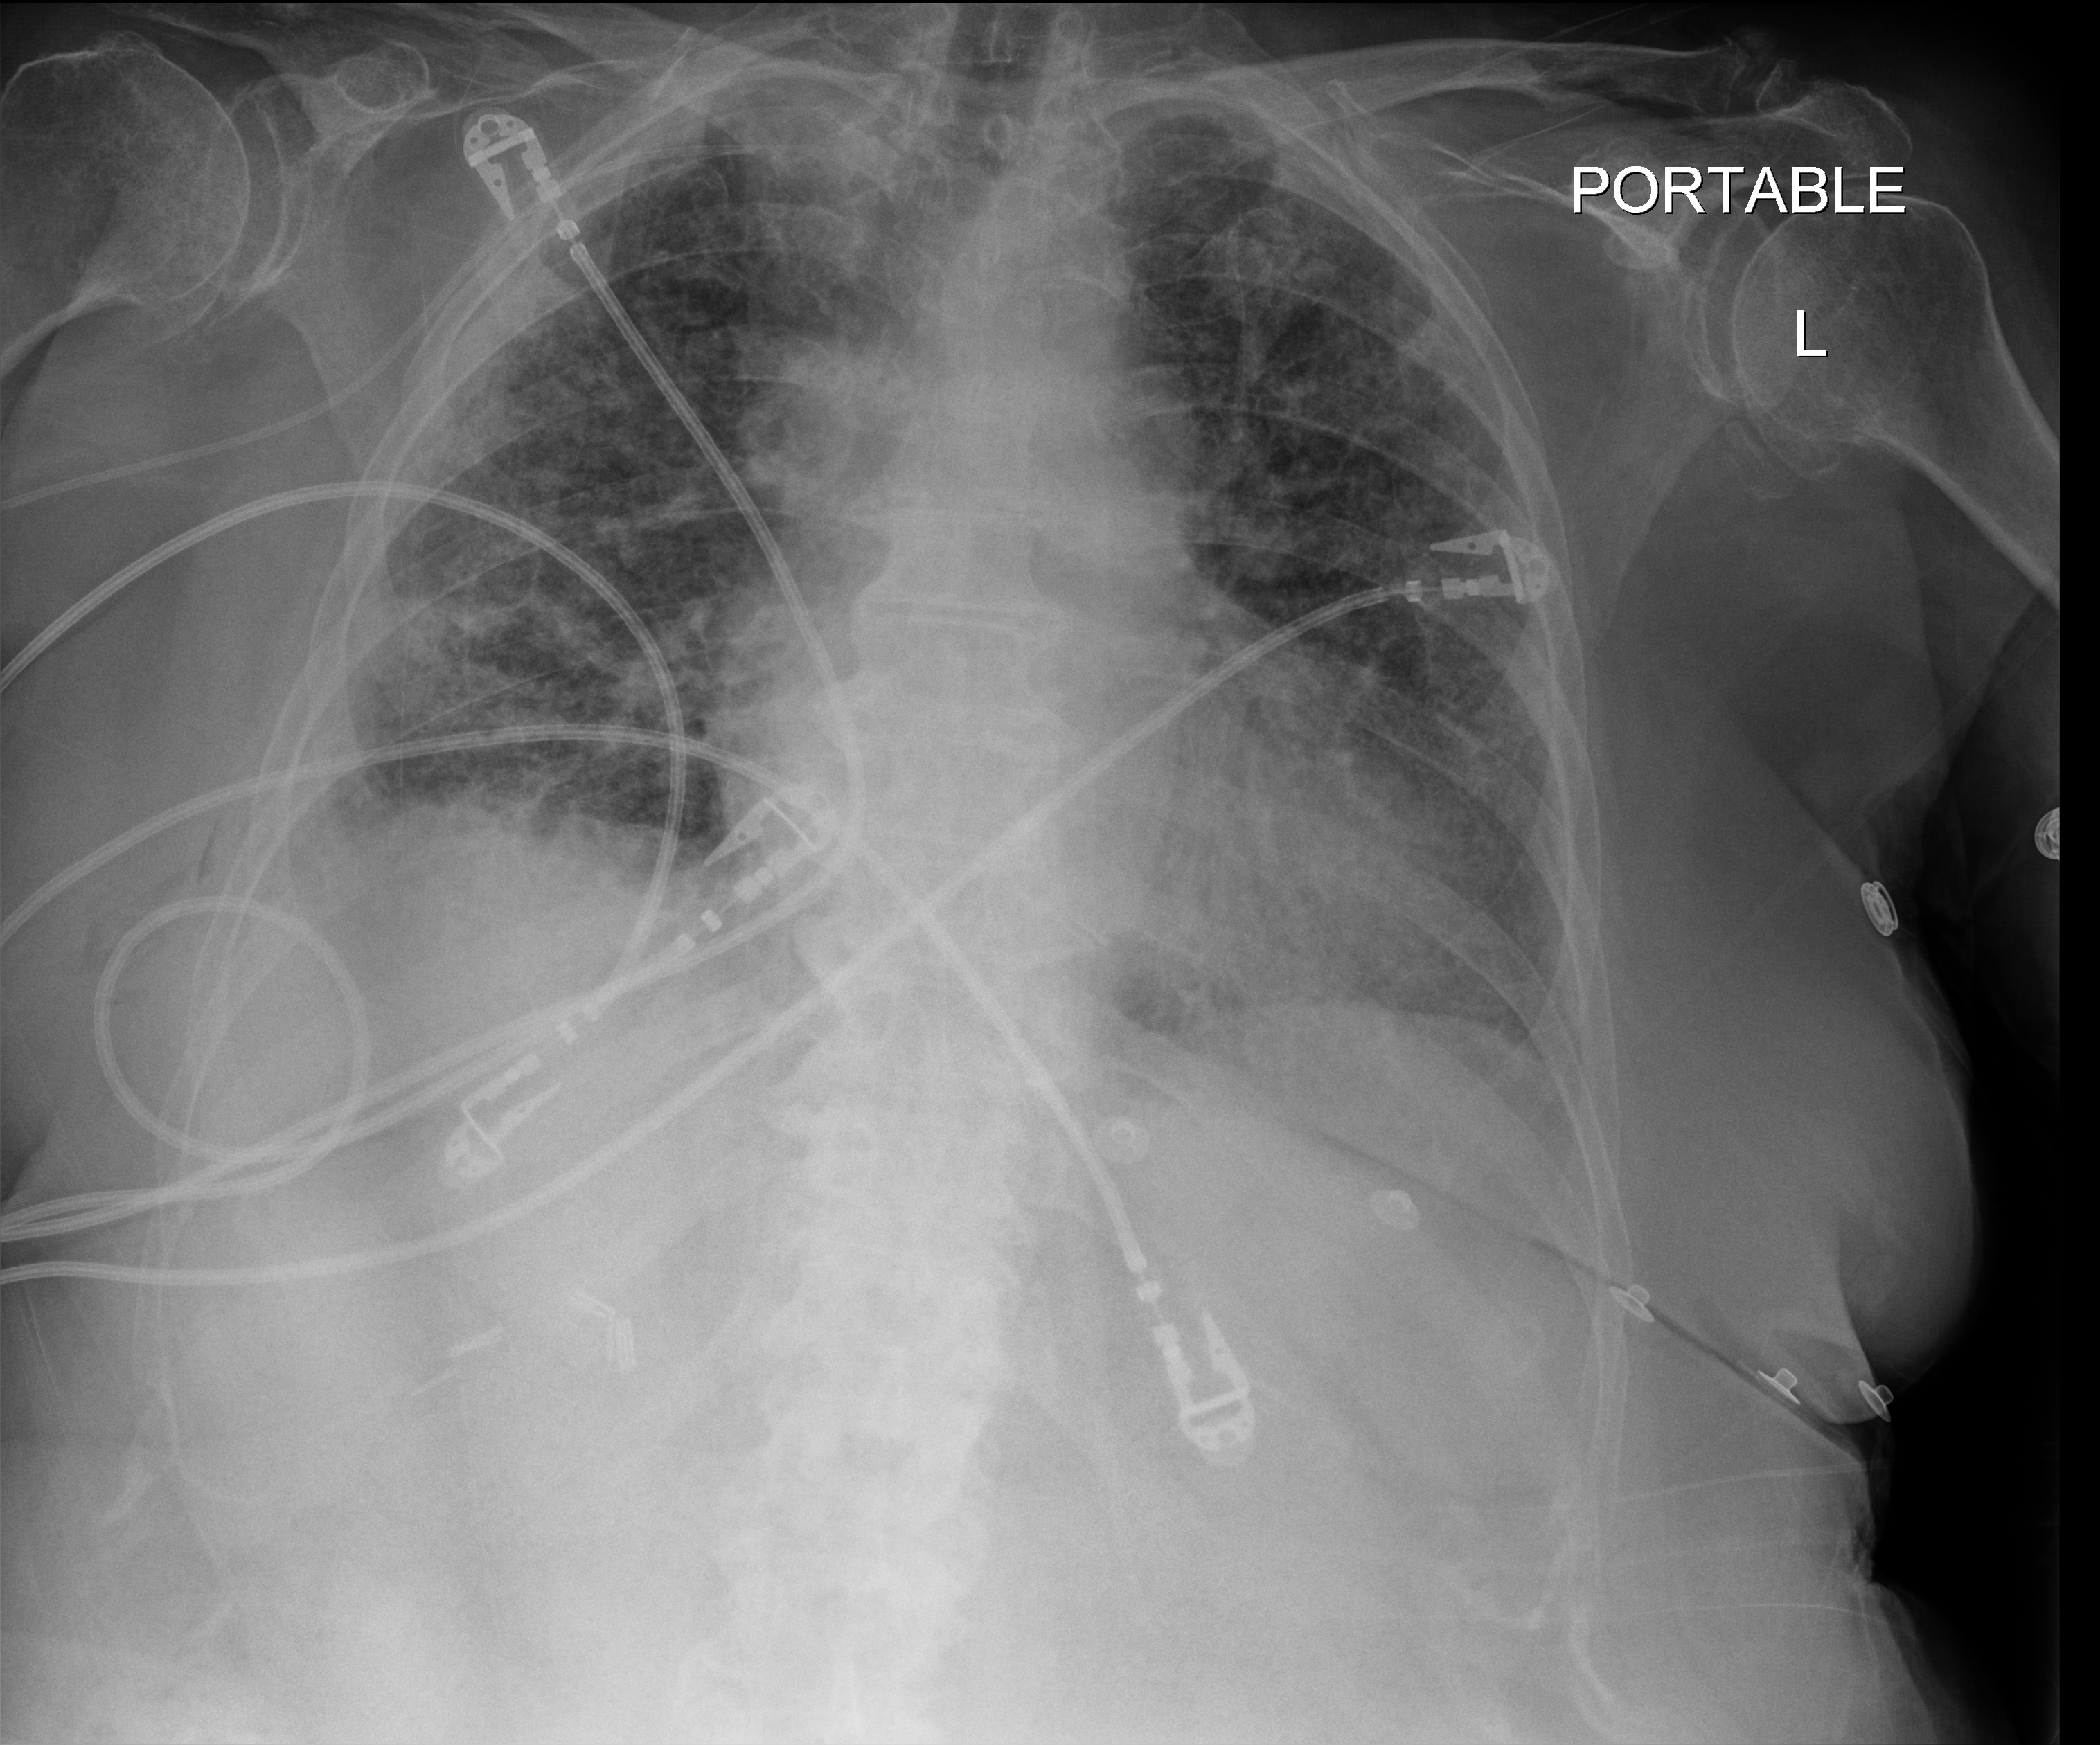
Chest X-ray (portable); anteroposterior (AP) projection. Patient hospitalised with COVID-19; female, aged 75–90 years.
From the hospital-stay record, not from the radiograph (when in the stay this image was taken is not recorded):
- admitted to intensive care during this hospital stay: no
- mechanically ventilated during this hospital stay: yes